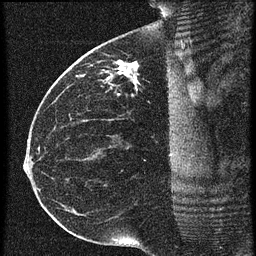
Breast MRI (dynamic contrast-enhanced), one sagittal slice; slice 31 of 60 in the series (ordered by position); 3 images stored at this slice position (order not interpretable as contrast timing); 1.5 T; TE 4.2 ms, TR 20.4 ms; 256 × 256 image matrix, field of view 200 × 200 mm. Female patient, age 35 years. Case-level facts recorded for this patient, not image findings: setting: breast cancer imaged before/during neoadjuvant chemotherapy; receptor status: HR-positive, HER2-negative.
Structures marked on this image (semi-automatic segmentation, software-assisted and operator-edited):
- analysis volume of interest (the breast-tissue region the enhancement analysis was run in; not a lesion): bounding box <84,50,179,97> (left, top, right, bottom; pixels)
- tumour enhancement mask (voxels above the 90 % enhancement threshold inside the analysis volume of interest): <118,62,139,85>